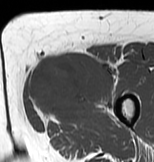
MRI of an extremity soft-tissue mass, one axial slice. Slice 26 of 83 in the series (ordered by position). MR volume resampled by the dataset authors to the PET/CT grid (not the native acquisition matrix). 154 × 162 image matrix. Female patient. Case-level facts recorded for this patient, not image findings: histological type: myxofibrosarcoma; grade: intermediate; site of the primary tumour: left thigh.
Outlined on this slice (expert contour drawn on MRI and transferred to this co-registered scan by the dataset authors):
- gross tumour volume including surrounding oedema: bounding box [x1, y1, x2, y2] px = [26, 50, 118, 122]
- gross tumour volume (mass): [28, 55, 114, 120]